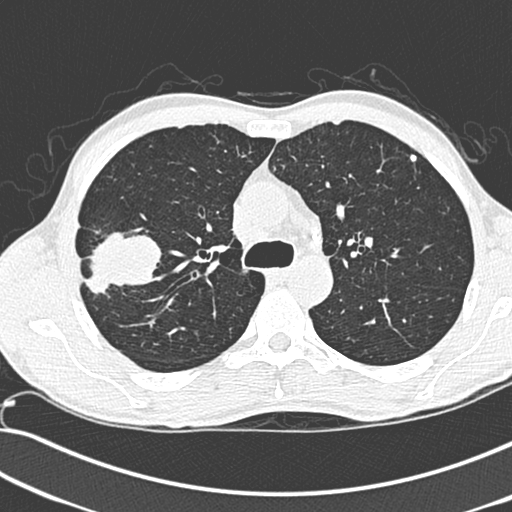
Low-dose screening chest CT, one axial slice; position 204 of 281 along the scan axis; lung window (W 1500 / L -600 HU); 512 × 512 image matrix, field of view 341 × 341 mm.
Outlined on this slice (outlined manually by an expert reader):
- lesion 1 (tumor, upper lobe of right lung): bounding box [x1, y1, x2, y2] px = [84, 232, 162, 298]